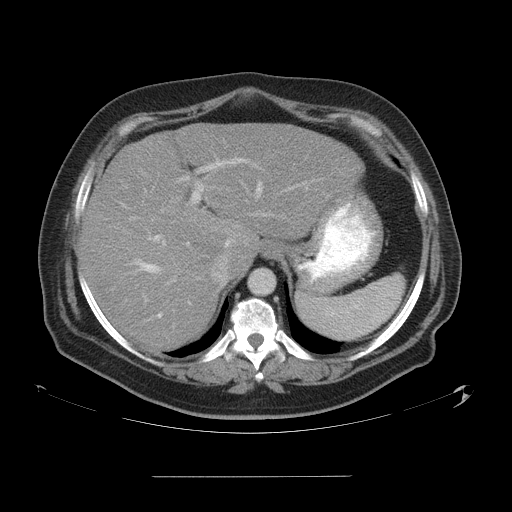
Contrast-enhanced abdominal CT, one axial slice; position 41 of 58 along the scan axis; 120 kVp; intravenous contrast given; soft-tissue window (W 400 / L 40 HU); 5 mm slice thickness; 512 × 512 image matrix. Male patient, age 63 years. From the clinical record (not read from this slice): diagnosis: colorectal cancer liver metastases, imaged before liver resection; multiple liver metastases: no; largest metastasis: 4.2 cm; disease in both lobes: no.
Annotated regions visible in this slice (outlined manually by an expert reader):
- hepatic veins: bounding box <122,177,299,318> (left, top, right, bottom; pixels)
- liver: <81,124,360,350>
- planned liver remnant (the part of the liver to remain after resection): <81,197,219,350>
- portal vein (with intrahepatic branches): <131,157,258,300>